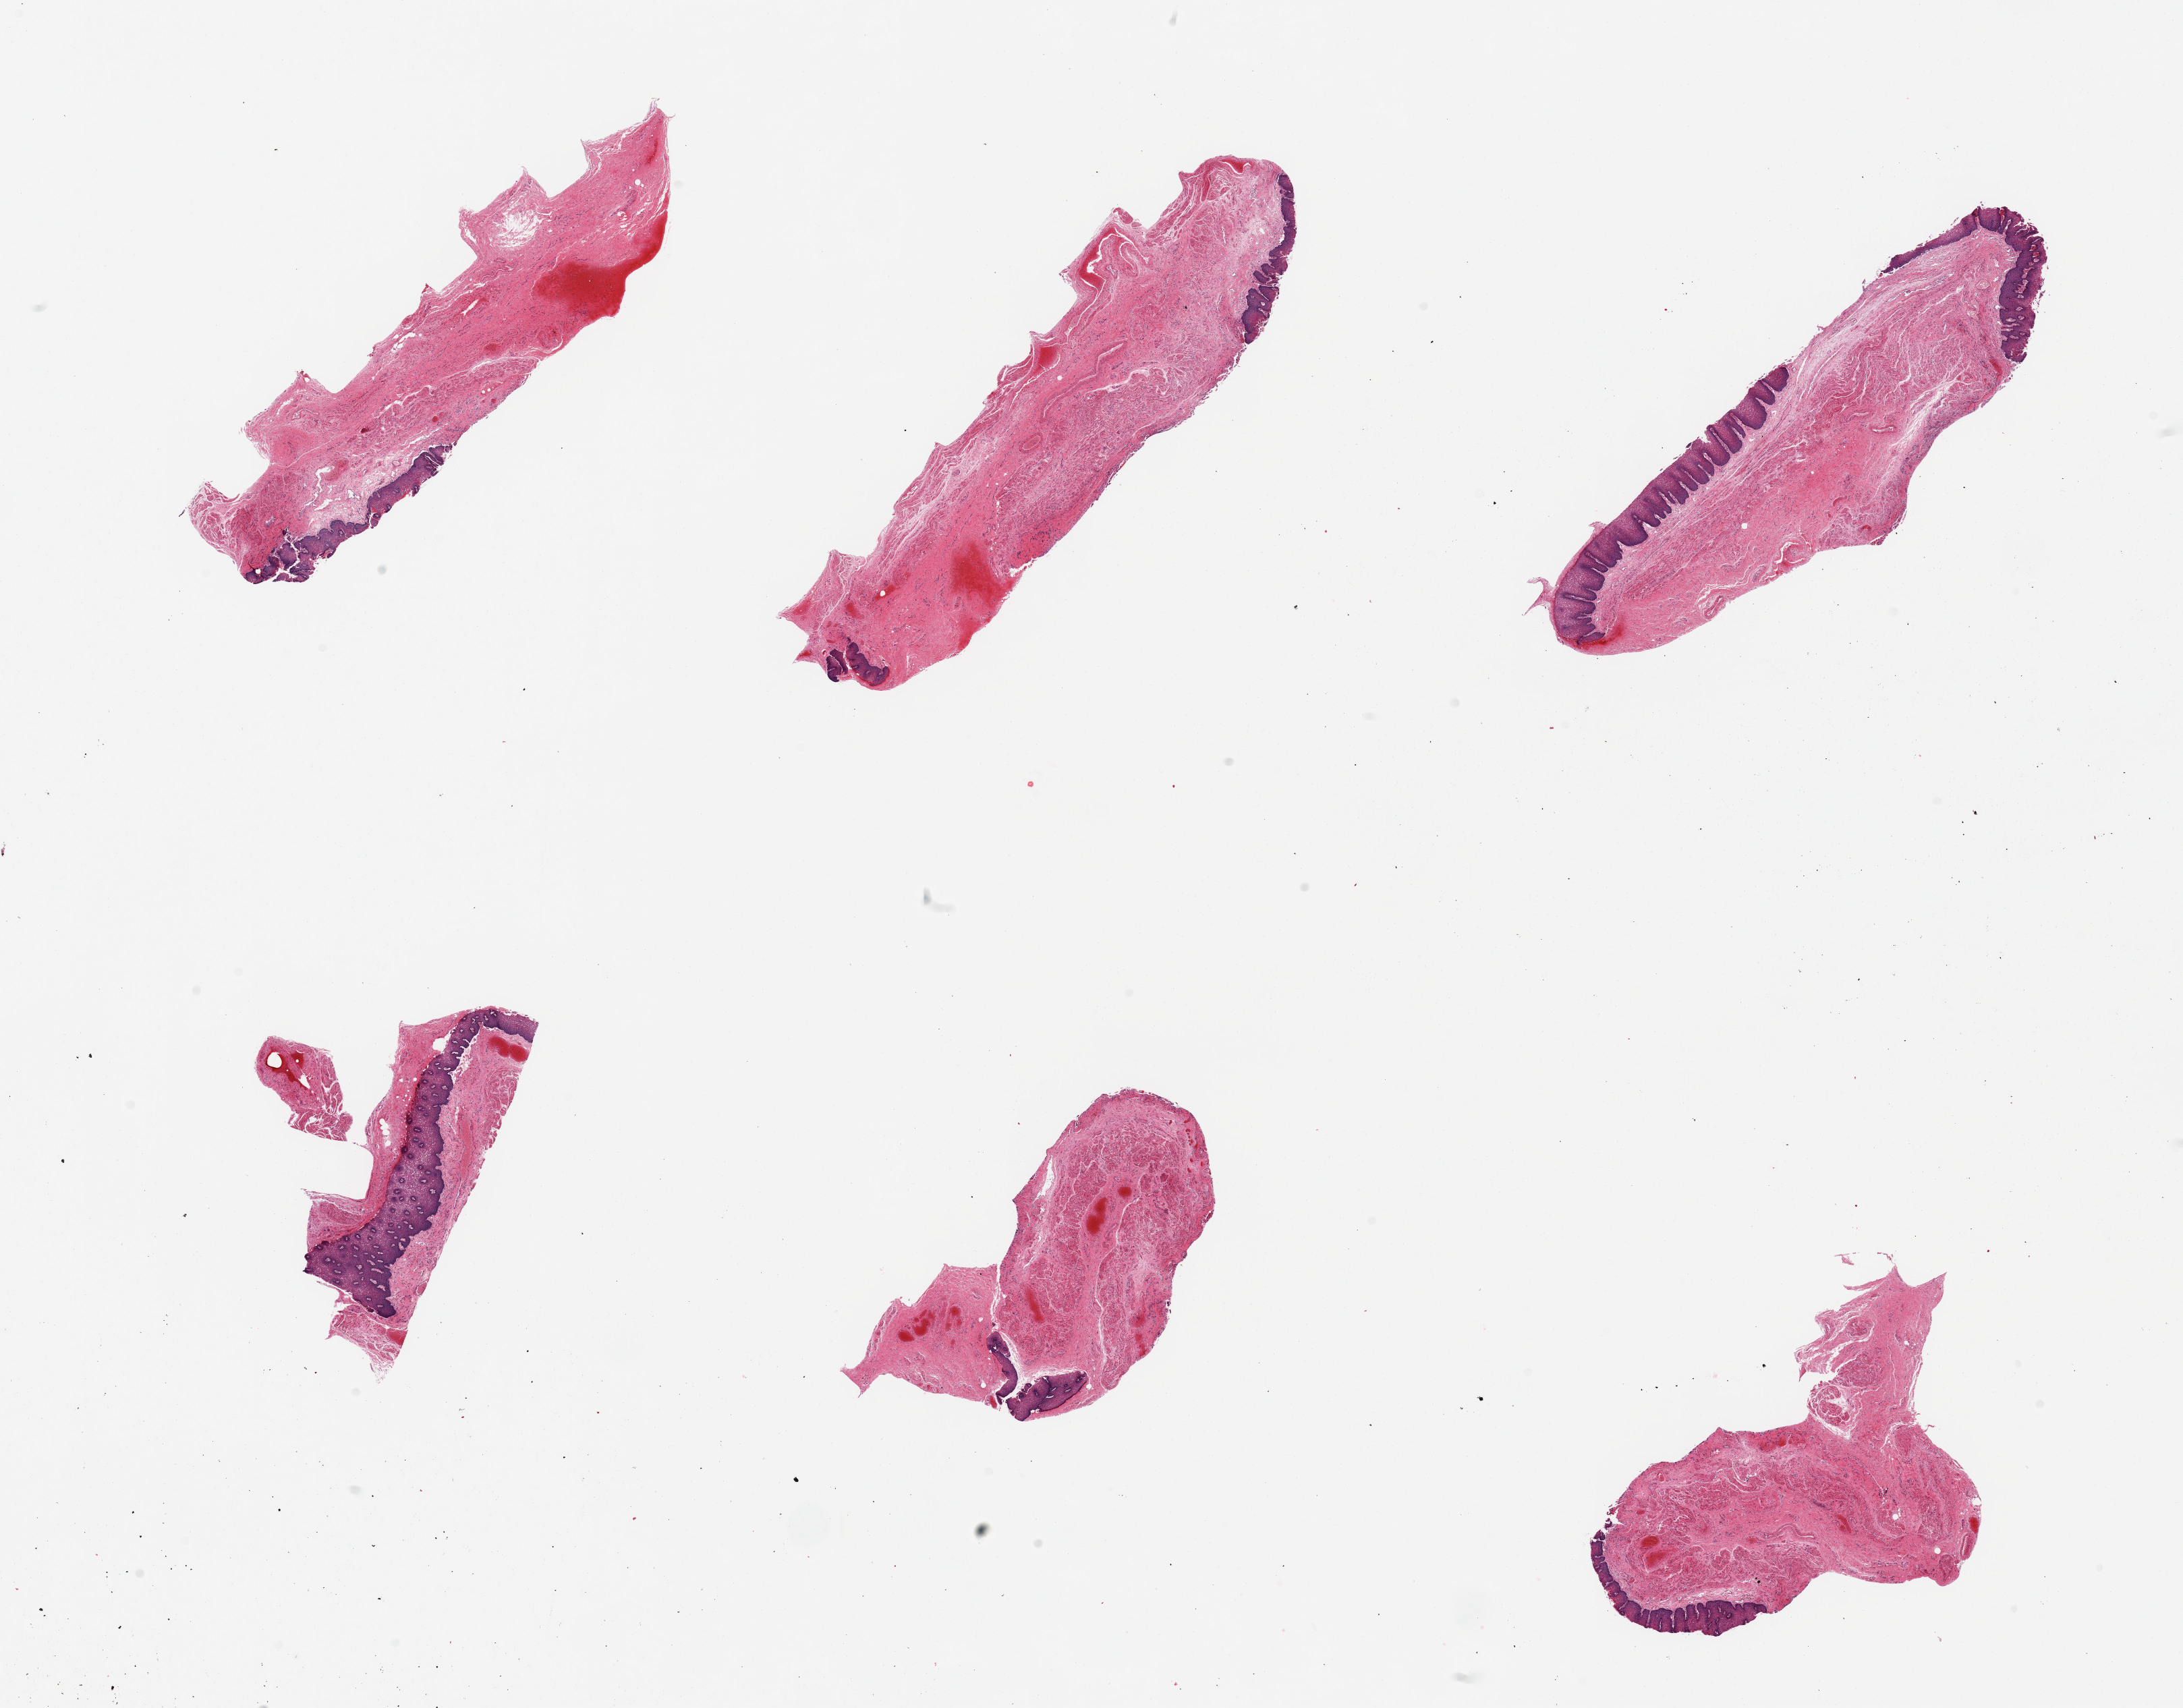
H&E whole-slide image, a low-resolution overview of the entire scanned area, about 25.6 x 20.0 mm (slide scanned at 20x); PAXgene-fixed, paraffin-embedded tissue; target tissue: esophageal mucous membrane; donor tissue sample. Donor: female.
Pathologist's review note for this sample: 6 pieces; squamous mucosa is incomplete, measures 0.42 mm thick.